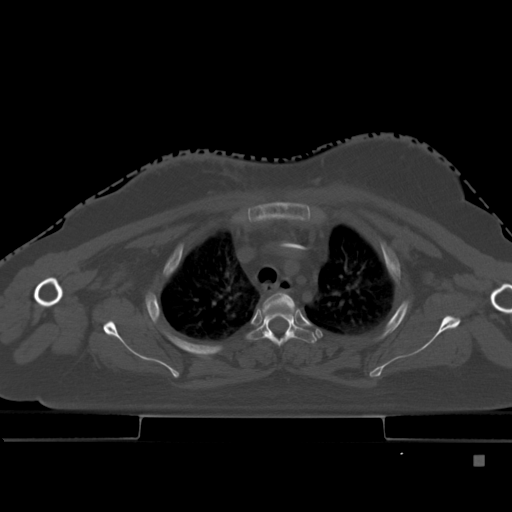
CT including the spine, one axial slice; position 349 of 495 along the scan axis; bone window (W 1800 / L 400 HU); 512 × 512 image matrix, field of view 404 × 404 mm. Patient: female, 33 years. Case-level facts recorded for this patient, not image findings: primary cancer: breast.
Annotated regions visible in this slice (semi-automatically segmented with operator editing):
- T2 vertebra: box from (x=263, y=291) to (x=295, y=309) px
- T3 vertebra: (x=248, y=313)–(x=318, y=347)